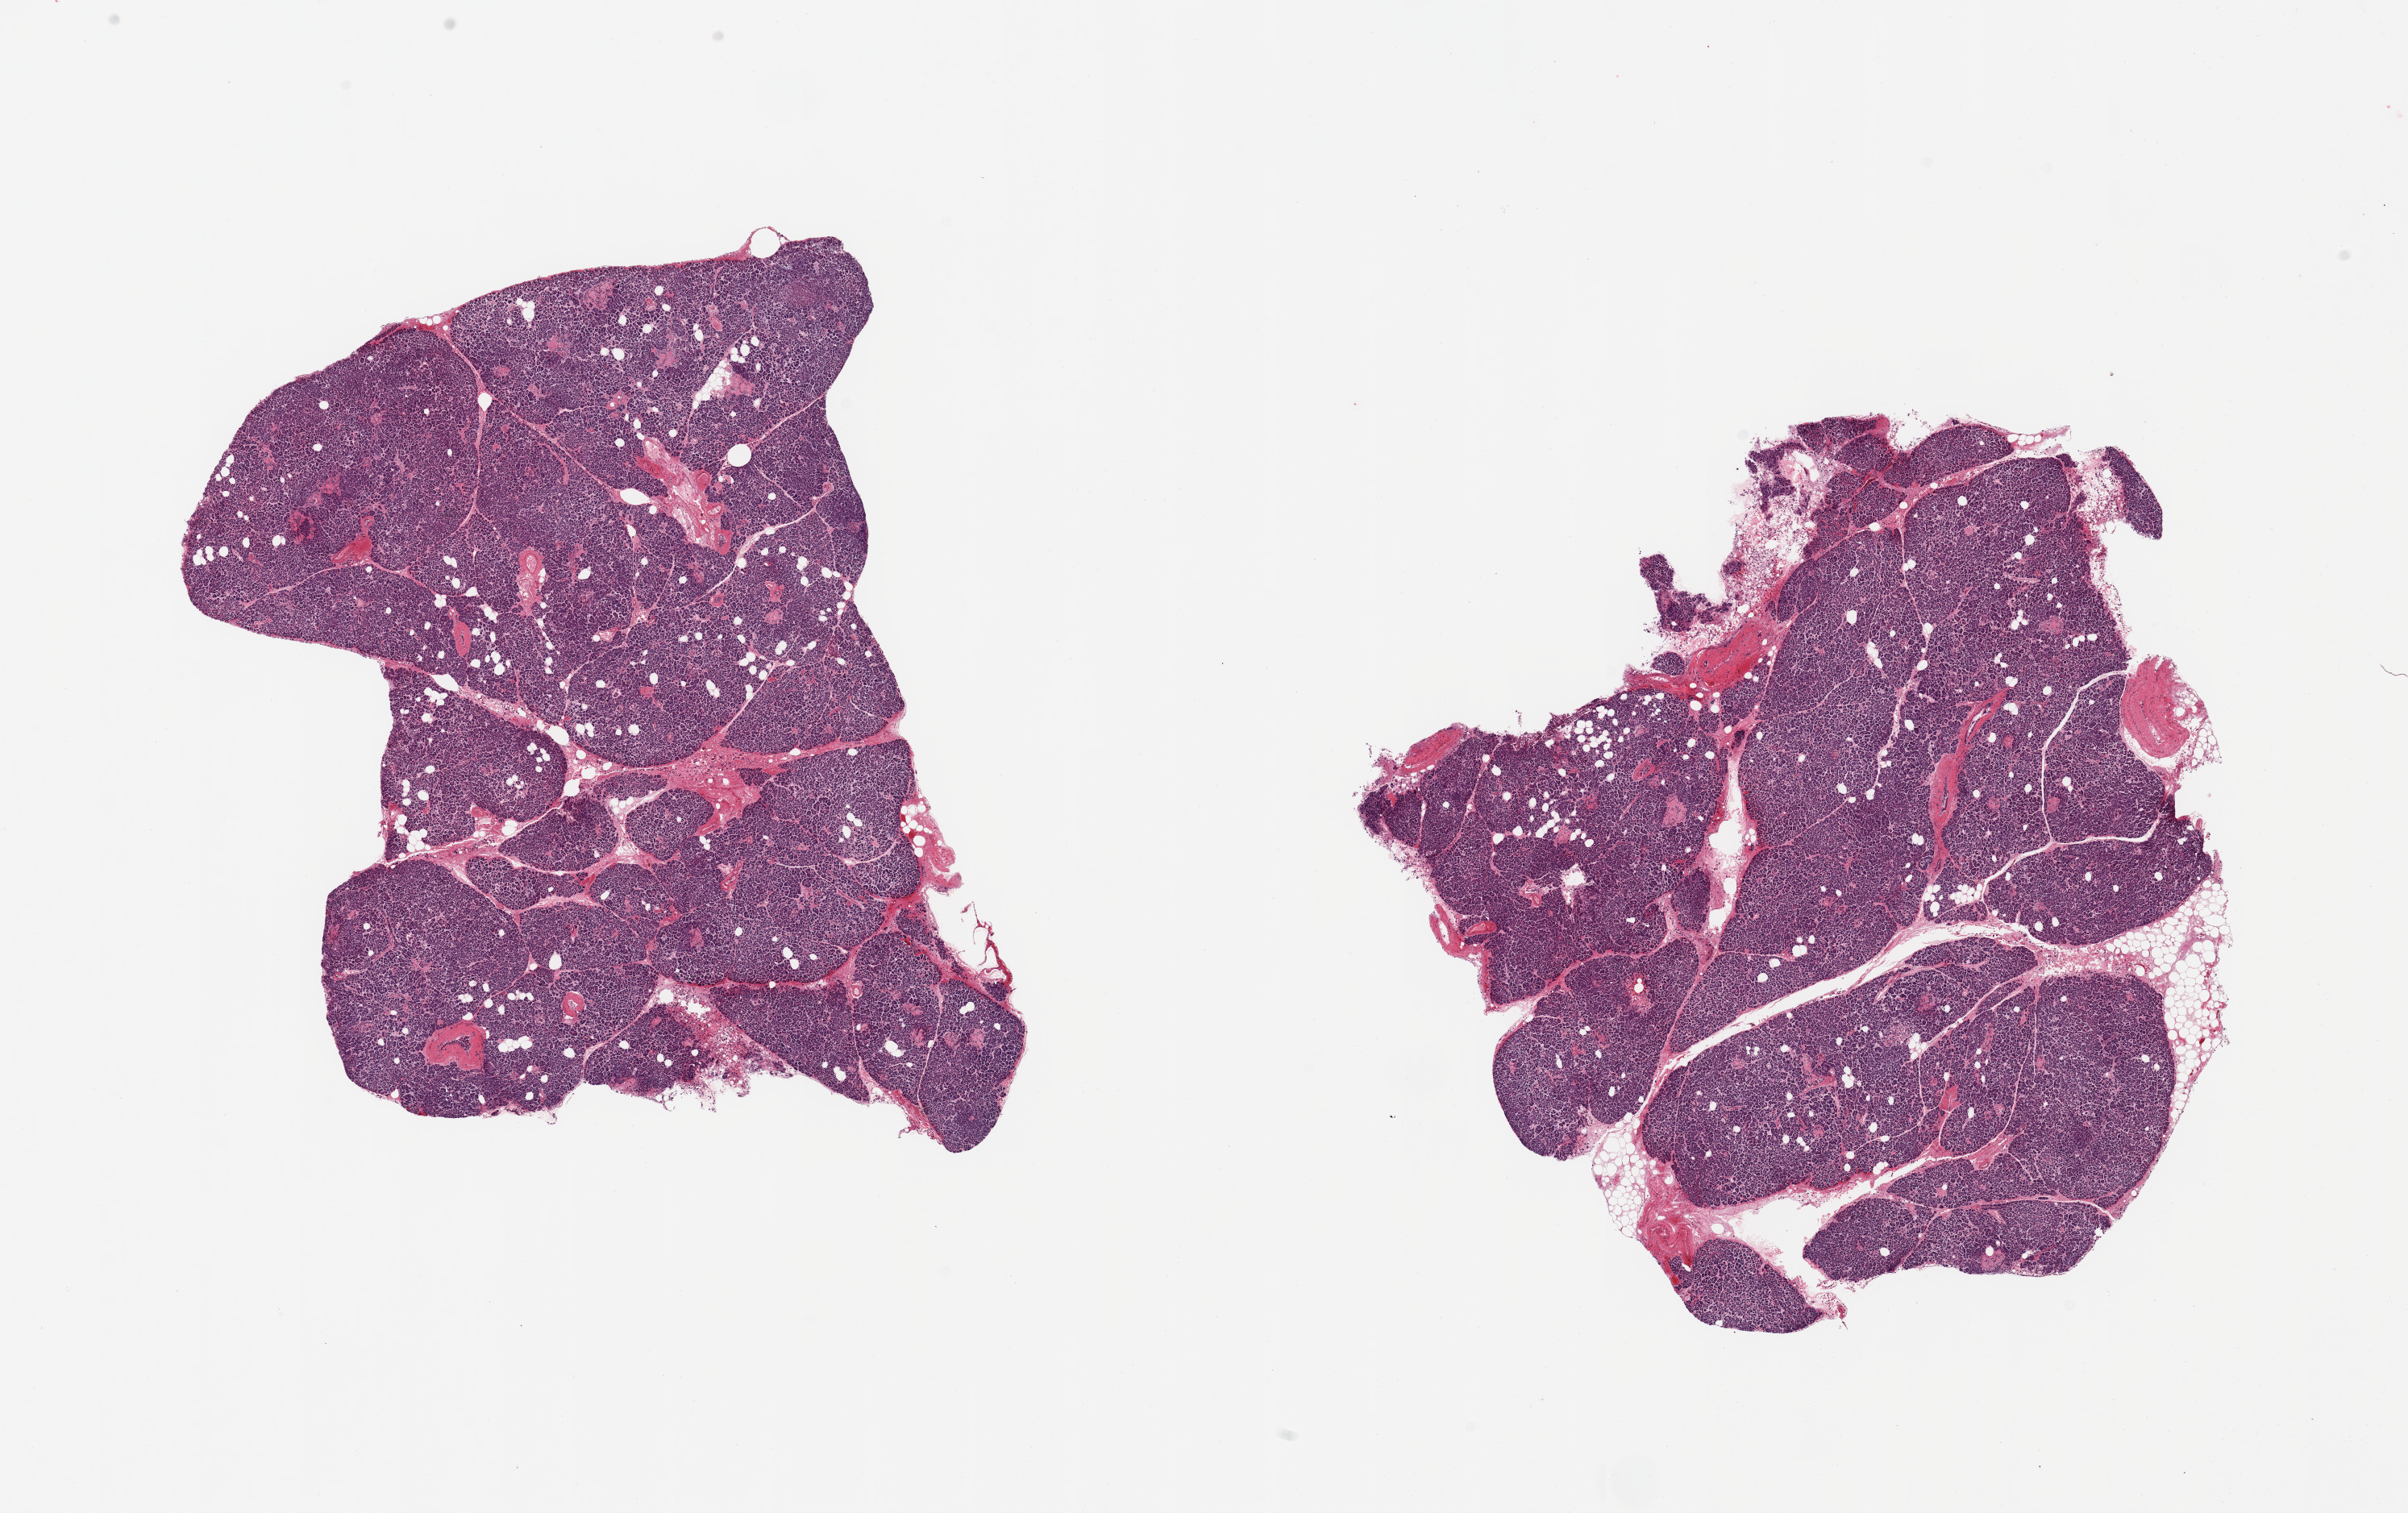
Whole-slide image, H&E stain, brightfield, low-resolution overview of the scanned area, about 23.6 x 14.8 mm (acquisition: 20x scan). PAXgene-fixed paraffin-embedded (PFPE) section. Sampled site (target tissue): pancreas. Tissue donor sample. Male donor.
Review note (as recorded): 2 pieces; severe sclerosis of islets (correlates with history of Diabetes type II).